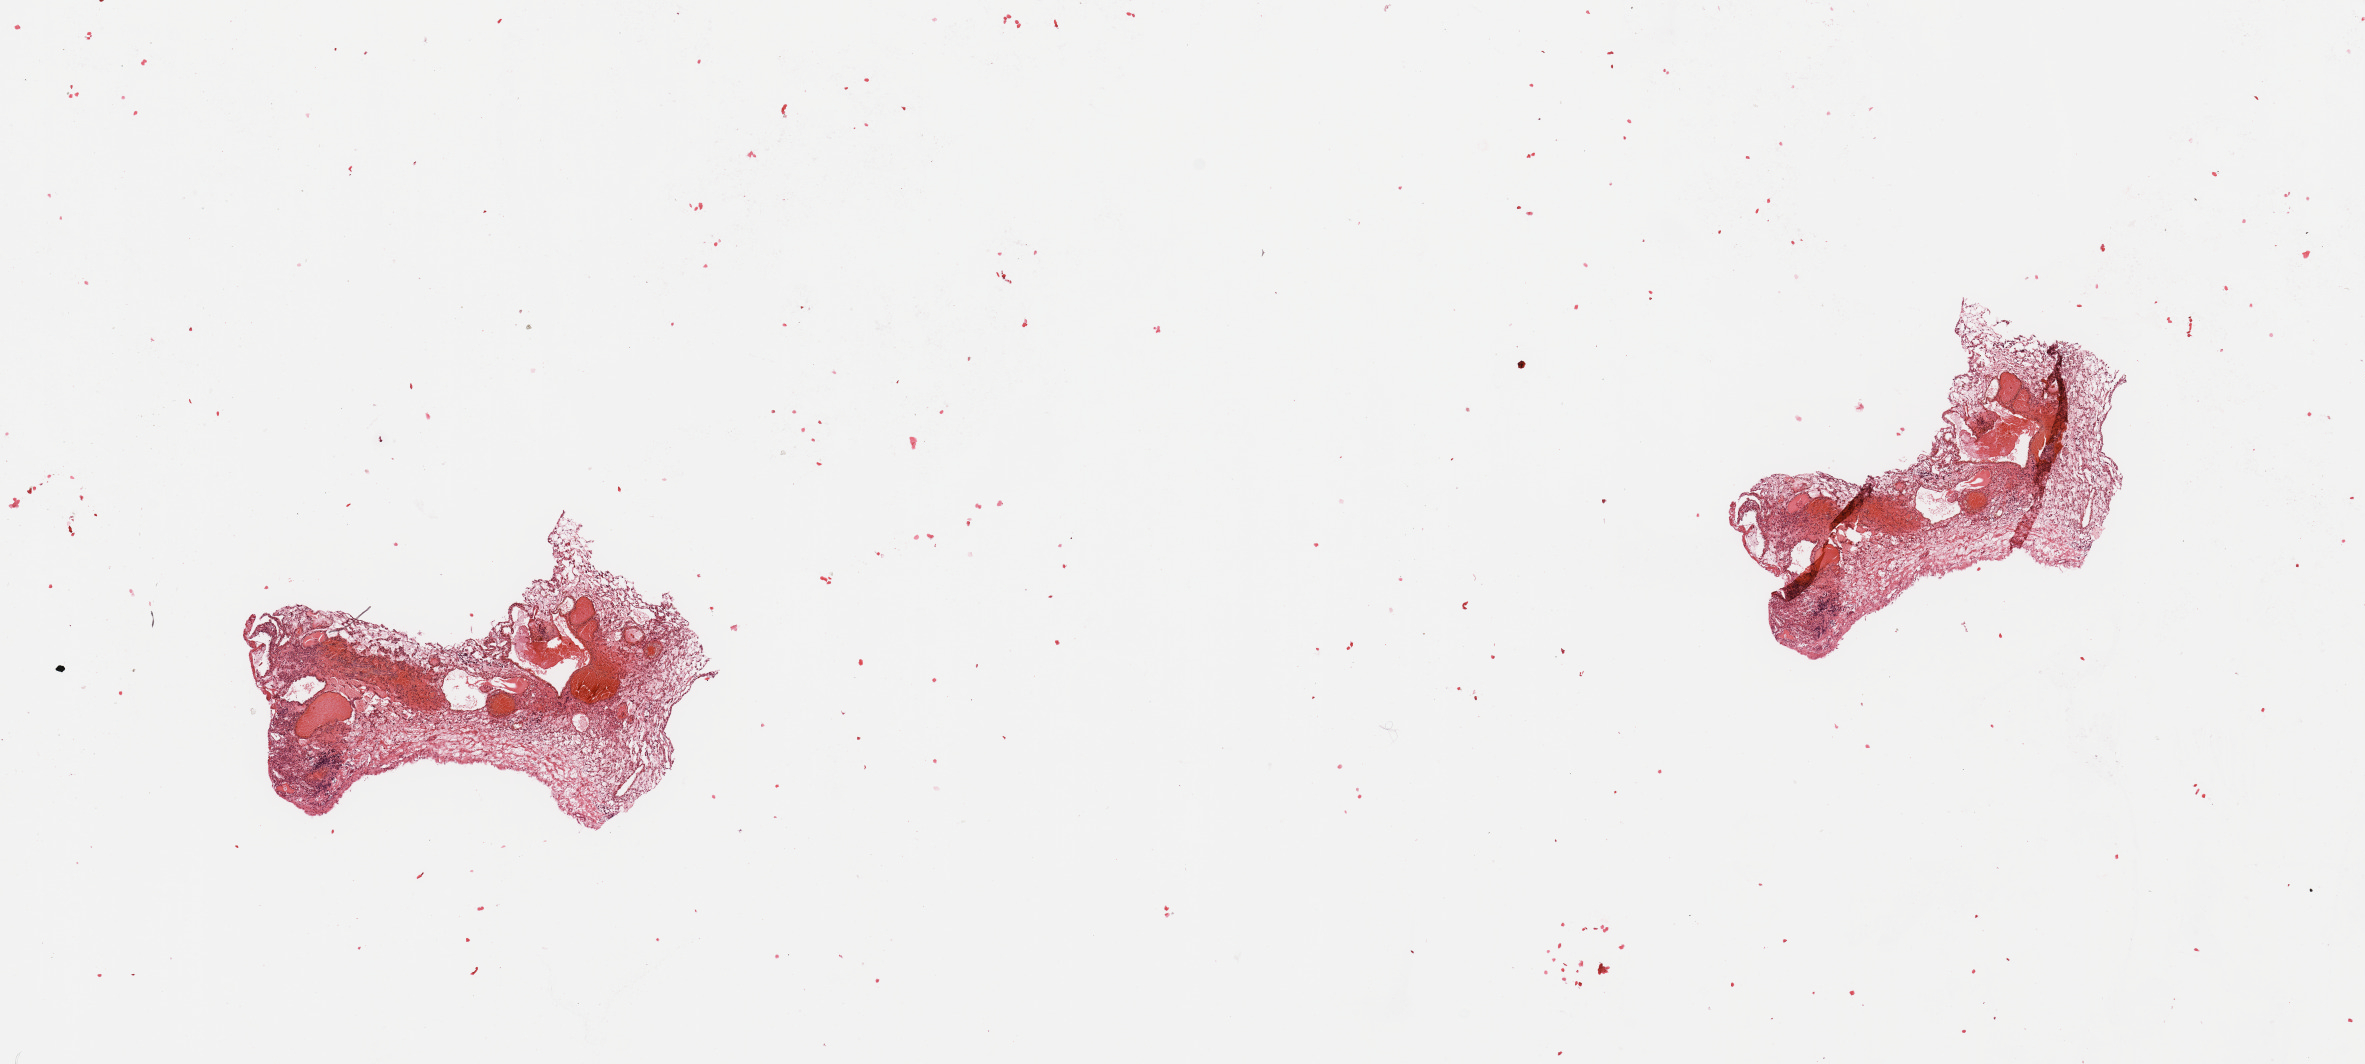
H&E whole-slide image — whole scanned area (about 18.7 x 8.4 mm, slide scanned at 20x) shown as a low-resolution overview, tumour tissue sample, sampled site: kidney. Male, 74 y/o. Histologic grade: G1 (well differentiated). Composition of this section per pathologist review: tumour nuclei 80%, necrosis 5%.
Primary tumour site (as recorded): middle. Diagnosis: Renal cell carcinoma, NOS. AJCC pathologic stage: I.